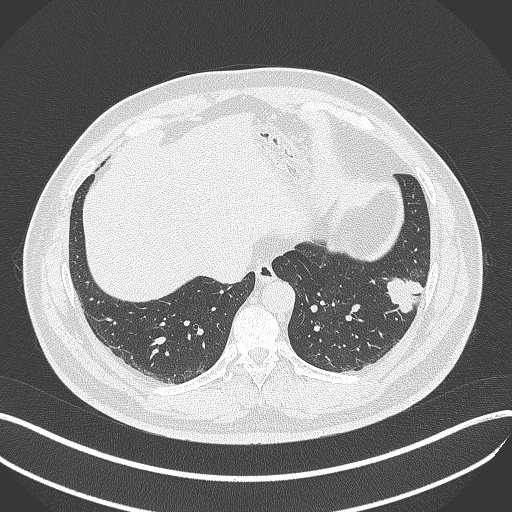
Chest CT, one axial slice; slice 118 of 429 in the series (ordered by position); 120 kVp; lung window (W 1500 / L -600 HU); 512 × 512 image matrix, field of view 400 × 400 mm. Patient: male, 39 years. From the clinical record (not read from this slice): clinical TNM (as recorded): T2a N0 M0; histopathological grade: G2-3.
Outlined on this slice (bounding box drawn by a radiologist):
- lung tumour (recorded histology: adenocarcinoma): bounding box (x1, y1, x2, y2) in pixels: (380, 270, 426, 318)